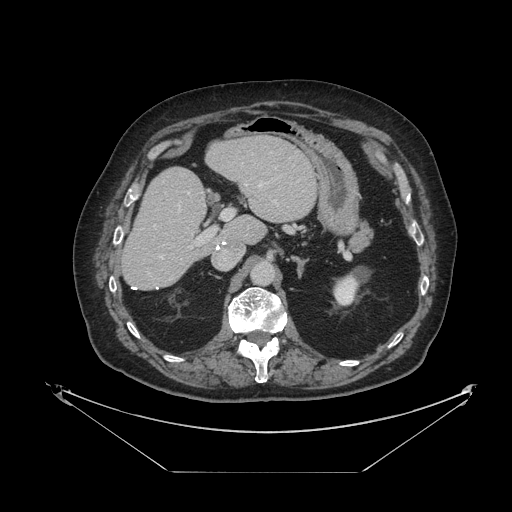
Contrast-enhanced abdominal CT, one axial slice; slice 59 of 121 in the series (ordered by position); 120 kVp; intravenous contrast given; soft-tissue window (W 400 / L 40 HU); 512 × 512 image matrix, field of view 500 × 500 mm. Male patient, age 68 years. From the clinical record (not read from this slice): diagnosis: colorectal cancer liver metastases, imaged before liver resection; multiple liver metastases: no; largest metastasis: 4 cm; disease in both lobes: no.
Annotated regions visible in this slice (manually delineated by an expert):
- hepatic veins: bounding box (x1, y1, x2, y2) in pixels: (161, 168, 276, 259)
- liver: (122, 136, 317, 290)
- planned liver remnant (the part of the liver to remain after resection): (122, 136, 317, 290)
- portal vein (with intrahepatic branches): (189, 182, 264, 248)